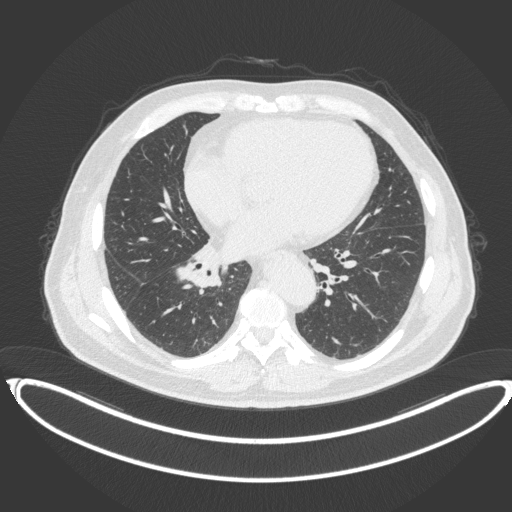
Chest CT, one axial slice; slice 171 of 383 in the series (ordered by position); reconstruction kernel B31f; 120 kVp; lung window (W 1500 / L -600 HU); 512 × 512 image matrix, field of view 448 × 448 mm. Patient: male, 61 years. From the clinical record (not read from this slice): clinical TNM (as recorded): T1b N1 M0.
Outlined on this slice (bounding box drawn by a radiologist):
- lung tumour (recorded histology: squamous cell carcinoma): bounding box (x1, y1, x2, y2) in pixels: (173, 254, 225, 289)